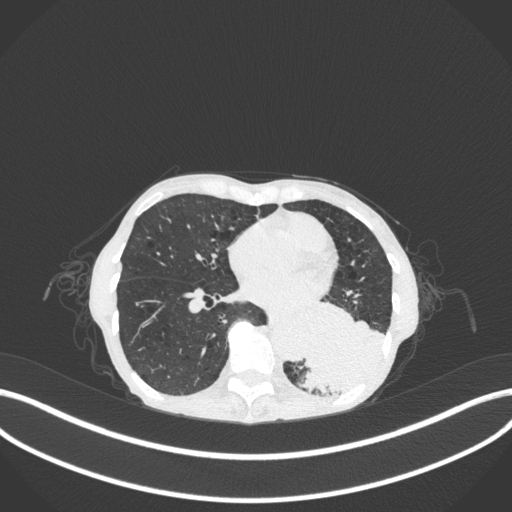
Chest CT, one axial slice. Position 108 of 347 along the scan axis. 120 kVp. Lung window (W 1500 / L -600 HU). 512 × 512 image matrix, field of view 400 × 400 mm. Patient: female, 70 years. Case-level facts recorded for this patient, not image findings: clinical TNM (as recorded): T3 N0 M0; histopathological grade: G3.
Annotated regions visible in this slice (bounding box drawn by a radiologist):
- lung tumour (recorded histology: small cell carcinoma): bounding box (x1, y1, x2, y2) in pixels: (294, 289, 390, 398)